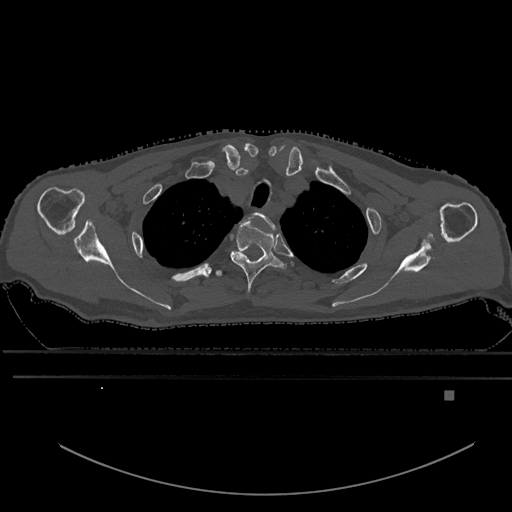
CT including the spine, one axial slice. Position 493 of 969 along the scan axis. Bone window (W 1800 / L 400 HU). 512 × 512 image matrix. Patient: male, 82 years. Case-level facts recorded for this patient, not image findings: primary cancer: prostate; vertebrae with lytic lesions (as recorded): T11, T9, T8, T2.
Outlined on this slice (semi-automatic segmentation, software-assisted and operator-edited):
- T1 vertebra: bounding box <254,213,275,229> (left, top, right, bottom; pixels)
- T2 vertebra: <230,219,287,295>
- T3 vertebra: <215,270,224,277>